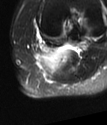
MRI of an extremity soft-tissue mass, one axial slice. Slice 52 of 78 in the series (ordered by position). T2-weighted fat-saturated. MR volume resampled by the dataset authors to the PET/CT grid (not the native acquisition matrix). 3.27 mm slice thickness. 107 × 125 image matrix. Female patient. From the clinical record (not read from this slice): histological type: extraskeletal high grade osteogenic sarcoma; grade: high; site of the primary tumour: left calf.
Structures marked on this image (expert contour drawn on MRI and transferred to this co-registered scan by the dataset authors):
- gross tumour volume (mass): bounding box [x1, y1, x2, y2] px = [42, 50, 68, 73]